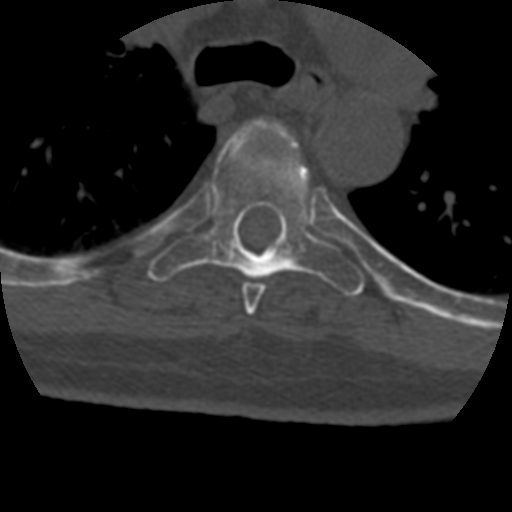
CT including the spine, one axial slice; slice 306 of 399 in the series (ordered by position); 120 kVp; bone window (W 1800 / L 400 HU); 1.25 mm slice thickness; 512 × 512 image matrix, field of view 160 × 160 mm. Patient age 69 years. From the clinical record (not read from this slice): primary cancer: prostate.
Outlined on this slice (semi-automatic segmentation, software-assisted and operator-edited):
- T5 vertebra: bounding box [x1, y1, x2, y2] px = [242, 123, 298, 316]
- T6 vertebra: [149, 123, 365, 296]